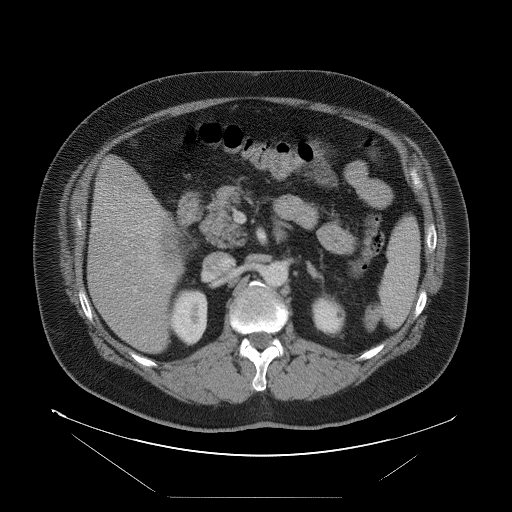
Contrast-enhanced abdominal CT, one axial slice. Position 44 of 114 along the scan axis. 120 kVp. Intravenous contrast given. Soft-tissue window (W 400 / L 40 HU). 5 mm slice thickness. 512 × 512 image matrix. Male patient, age 61 years. From the clinical record (not read from this slice): diagnosis: colorectal cancer liver metastases, imaged before liver resection; multiple liver metastases: no; largest metastasis: 6.5 cm.
Structures marked on this image (outlined manually by an expert reader):
- liver: bounding box (x1, y1, x2, y2) in pixels: (89, 157, 185, 353)
- liver metastasis: (162, 218, 182, 261)